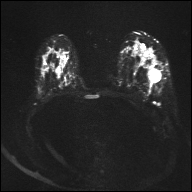
Breast MRI, one axial slice. Position 21 of 32 along the scan axis. Diffusion-weighted series; image 2 of 4 stored at this slice position (different b-values; order by instance number). 1.5 T. 4 mm slice thickness. 192 × 192 image matrix, field of view 360 × 360 mm. Female patient.
Outlined on this slice (outlined manually by an expert reader):
- tumour on diffusion-weighted imaging: bounding box (x1, y1, x2, y2) in pixels: (150, 70, 158, 79)